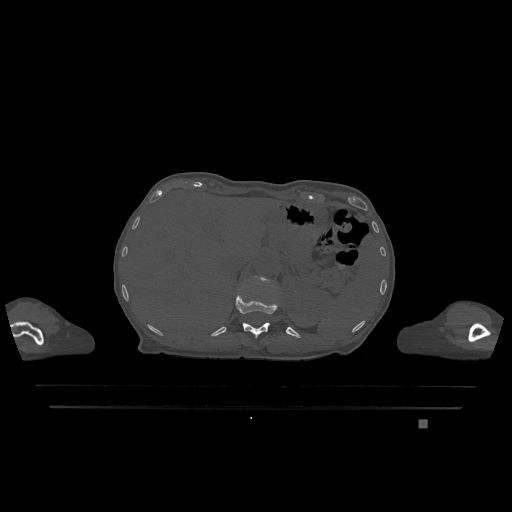
CT including the spine, one axial slice. Bone window (W 1800 / L 400 HU). 512 × 512 image matrix. Female patient, age 74 years. Case-level facts recorded for this patient, not image findings: primary cancer: lung.
Structures marked on this image (semi-automatically segmented with operator editing):
- L1 vertebra: bounding box [x1, y1, x2, y2] px = [255, 277, 270, 283]
- T12 vertebra: [235, 293, 278, 338]